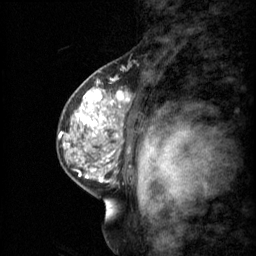
Breast MRI (dynamic contrast-enhanced), one sagittal slice. Position 42 of 60 along the scan axis. 3 images stored at this slice position (order not interpretable as contrast timing). 1.5 T. TE 4.2 ms, TR 11 ms. 2 mm slice thickness. 256 × 256 image matrix, field of view 200 × 200 mm. Patient: female, 48 years.
Annotated regions visible in this slice (semi-automatically segmented with operator editing):
- analysis volume of interest (the breast-tissue region the enhancement analysis was run in; not a lesion): box from (x=69, y=74) to (x=140, y=147) px
- tumour enhancement mask (voxels above the 70 % enhancement threshold inside the analysis volume of interest): (x=80, y=88)–(x=130, y=139)